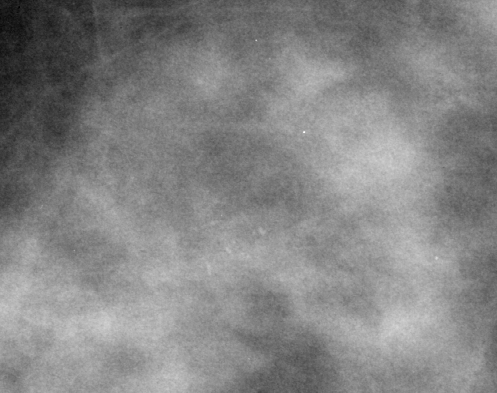
Cropped region of a digitized screen-film mammogram centred on a radiologist-marked abnormality; right breast; MLO view.
Marked abnormality: calcifications, morphology pleomorphic, distribution clustered; BI-RADS assessment category 4; subtlety rating 2 on a 1 (subtle) to 5 (obvious) scale; pathology result (as recorded, not read from the image): benign.